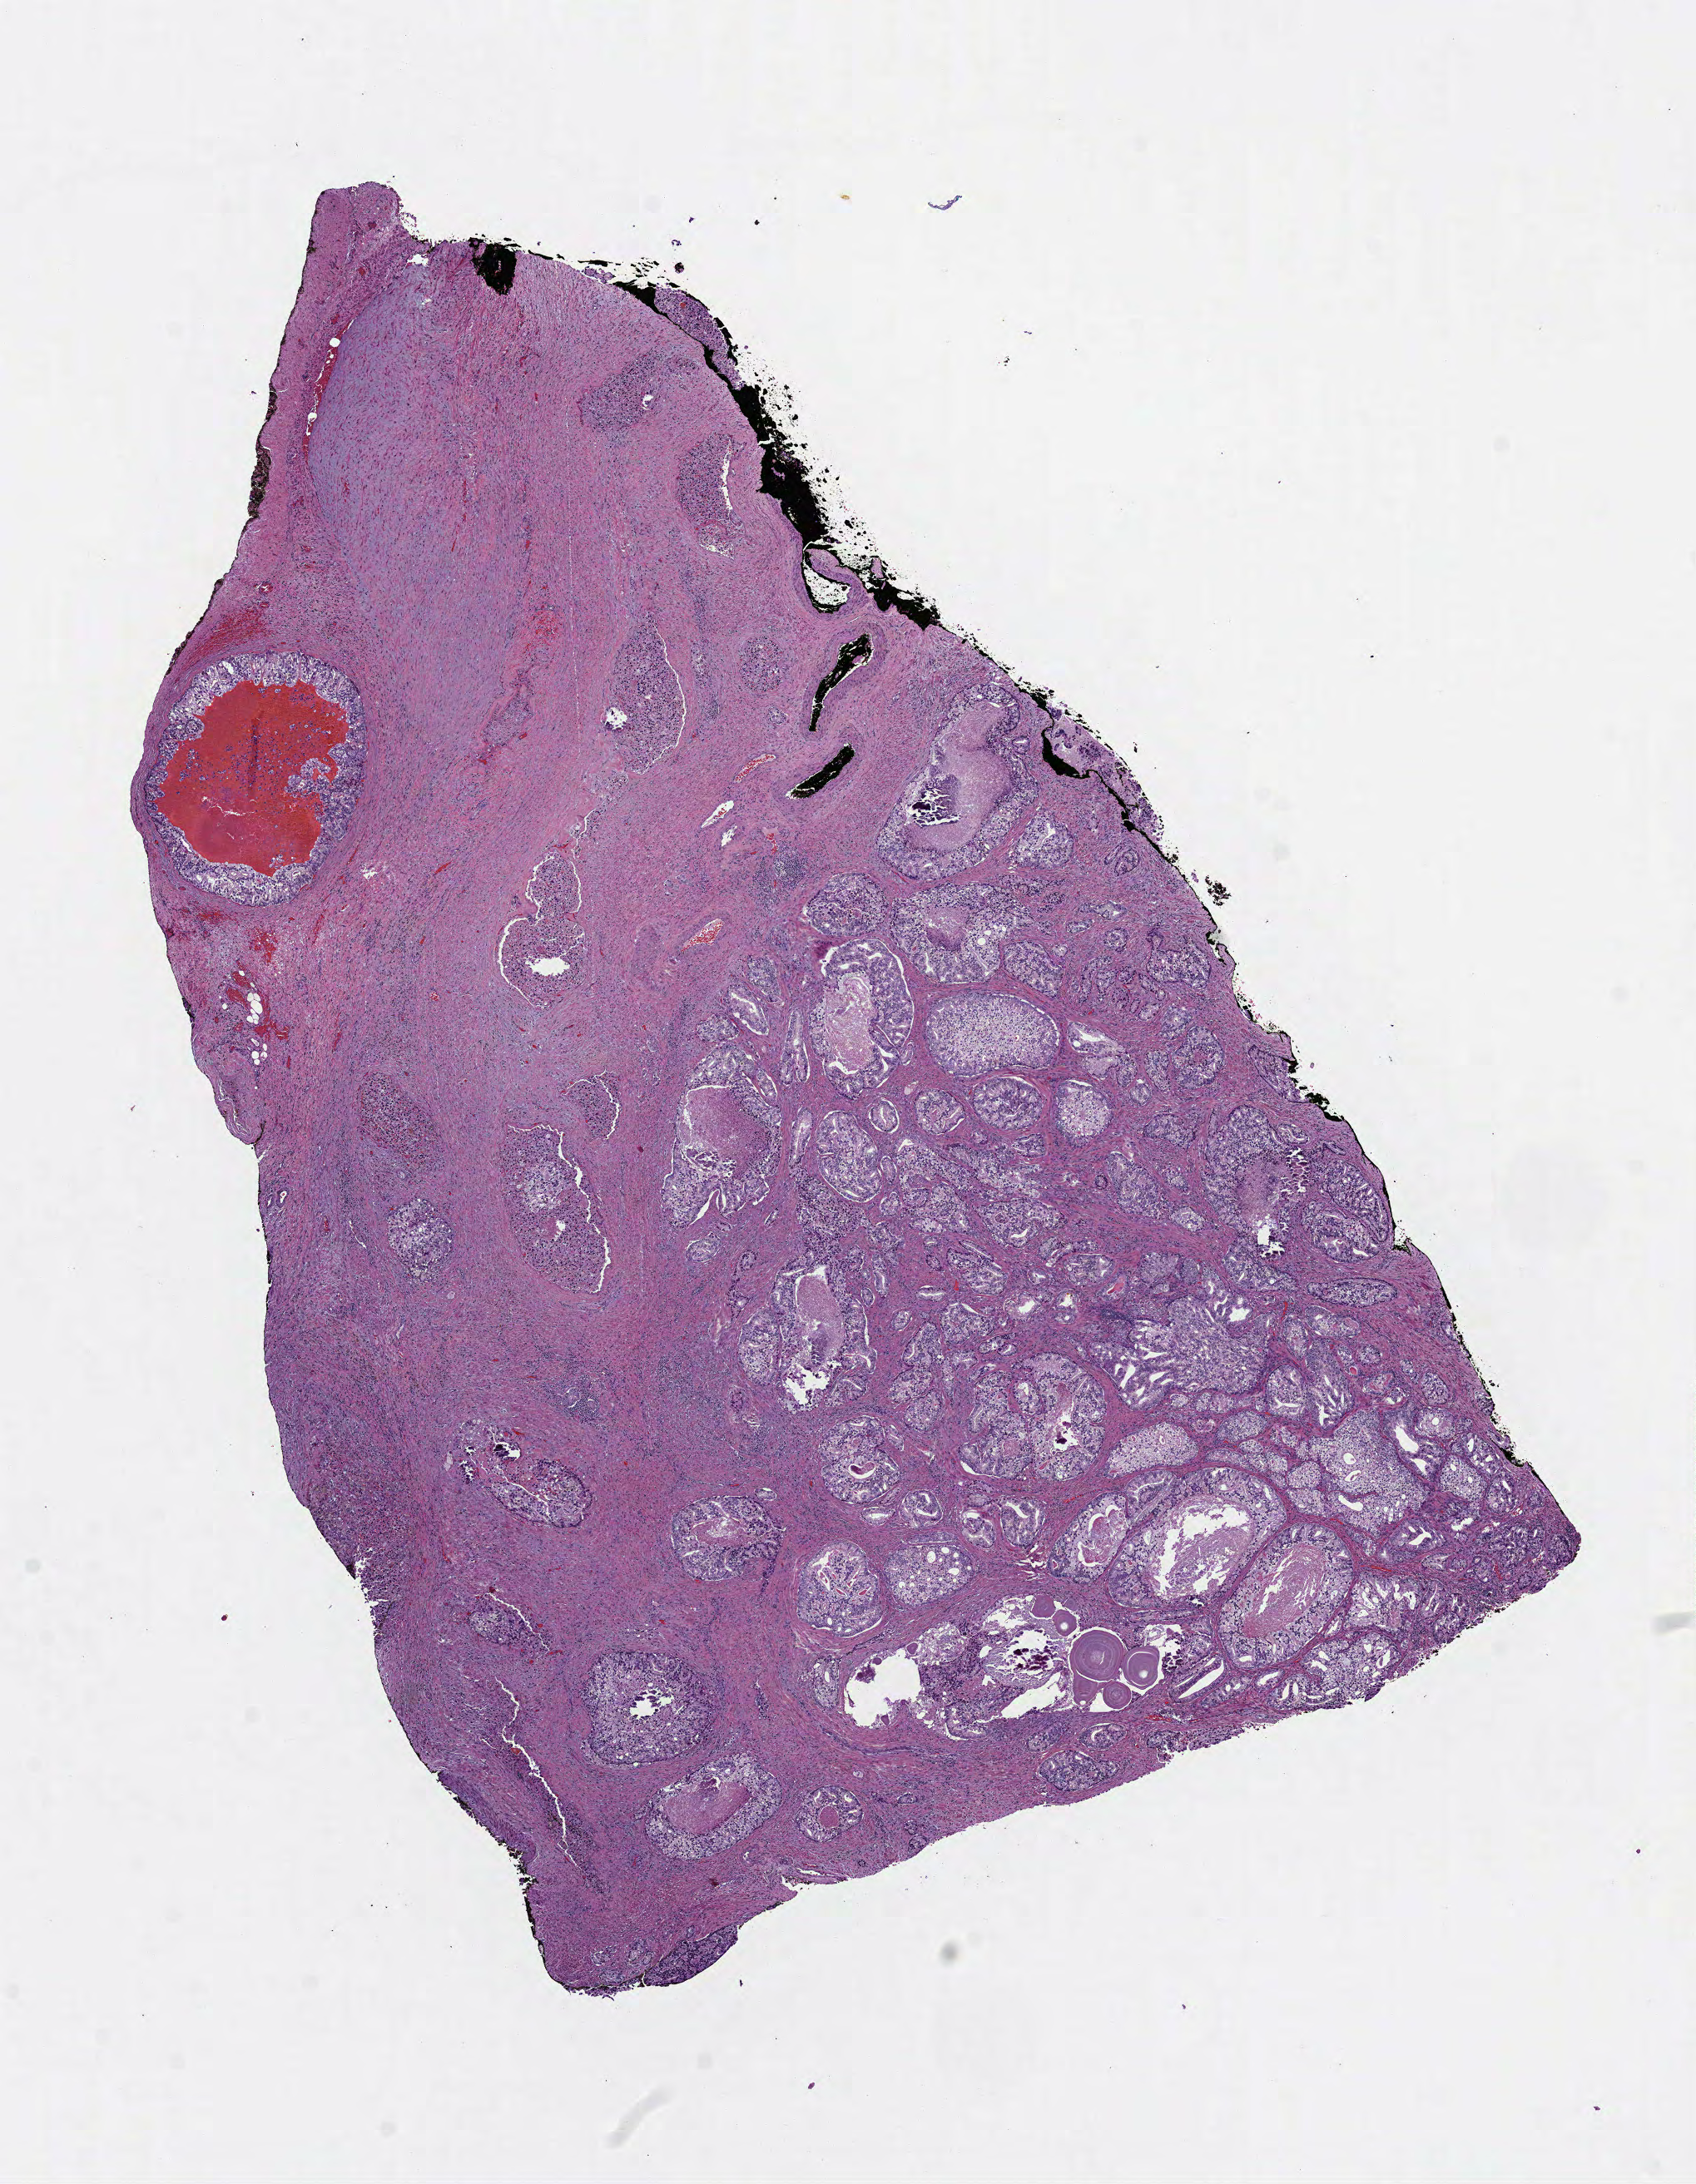
Whole-slide histology image, H&E-stained, low-resolution overview of the scanned area, about 8.2 x 10.6 mm. Formalin-fixed paraffin-embedded (FFPE) diagnostic section. Sample: primary tumour, prostate. Male, age 58 years at initial diagnosis. Gleason score: 9 (5+4).
Lymph nodes positive (case pathology): 0 of 2 examined. Pathologic diagnosis: Adenocarcinoma, NOS (prostate gland).